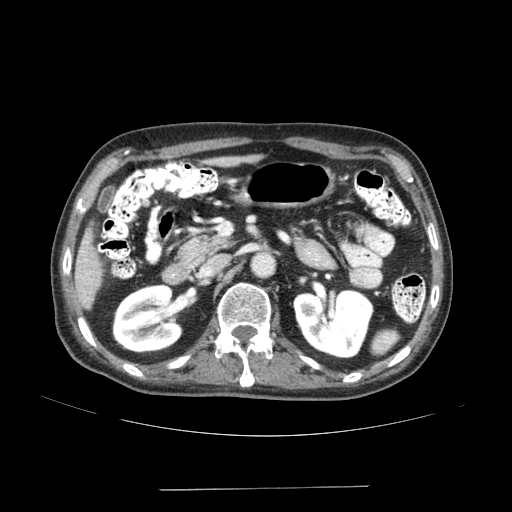
Contrast-enhanced abdominal CT (liver protocol), one axial slice. Slice 66 of 192 in the series (ordered by position). Reconstruction kernel SOFT. 120 kVp. Soft-tissue window (W 400 / L 40 HU). 2.5 mm slice thickness. 512 × 512 image matrix, field of view 400 × 400 mm. From the clinical record (not read from this slice): diagnosis: hepatocellular carcinoma (patient treated with transarterial chemoembolisation; whether this scan precedes or follows treatment is not stated here); TNM stage (as recorded): Stage-IVA; Child-Pugh class: A.
Annotated regions visible in this slice (semi-automatic segmentation, software-assisted and operator-edited):
- liver parenchyma outside the tumour (the mass and vessels are separate outlines, so this box may not span the whole liver): bounding box [x1, y1, x2, y2] px = [74, 227, 102, 308]